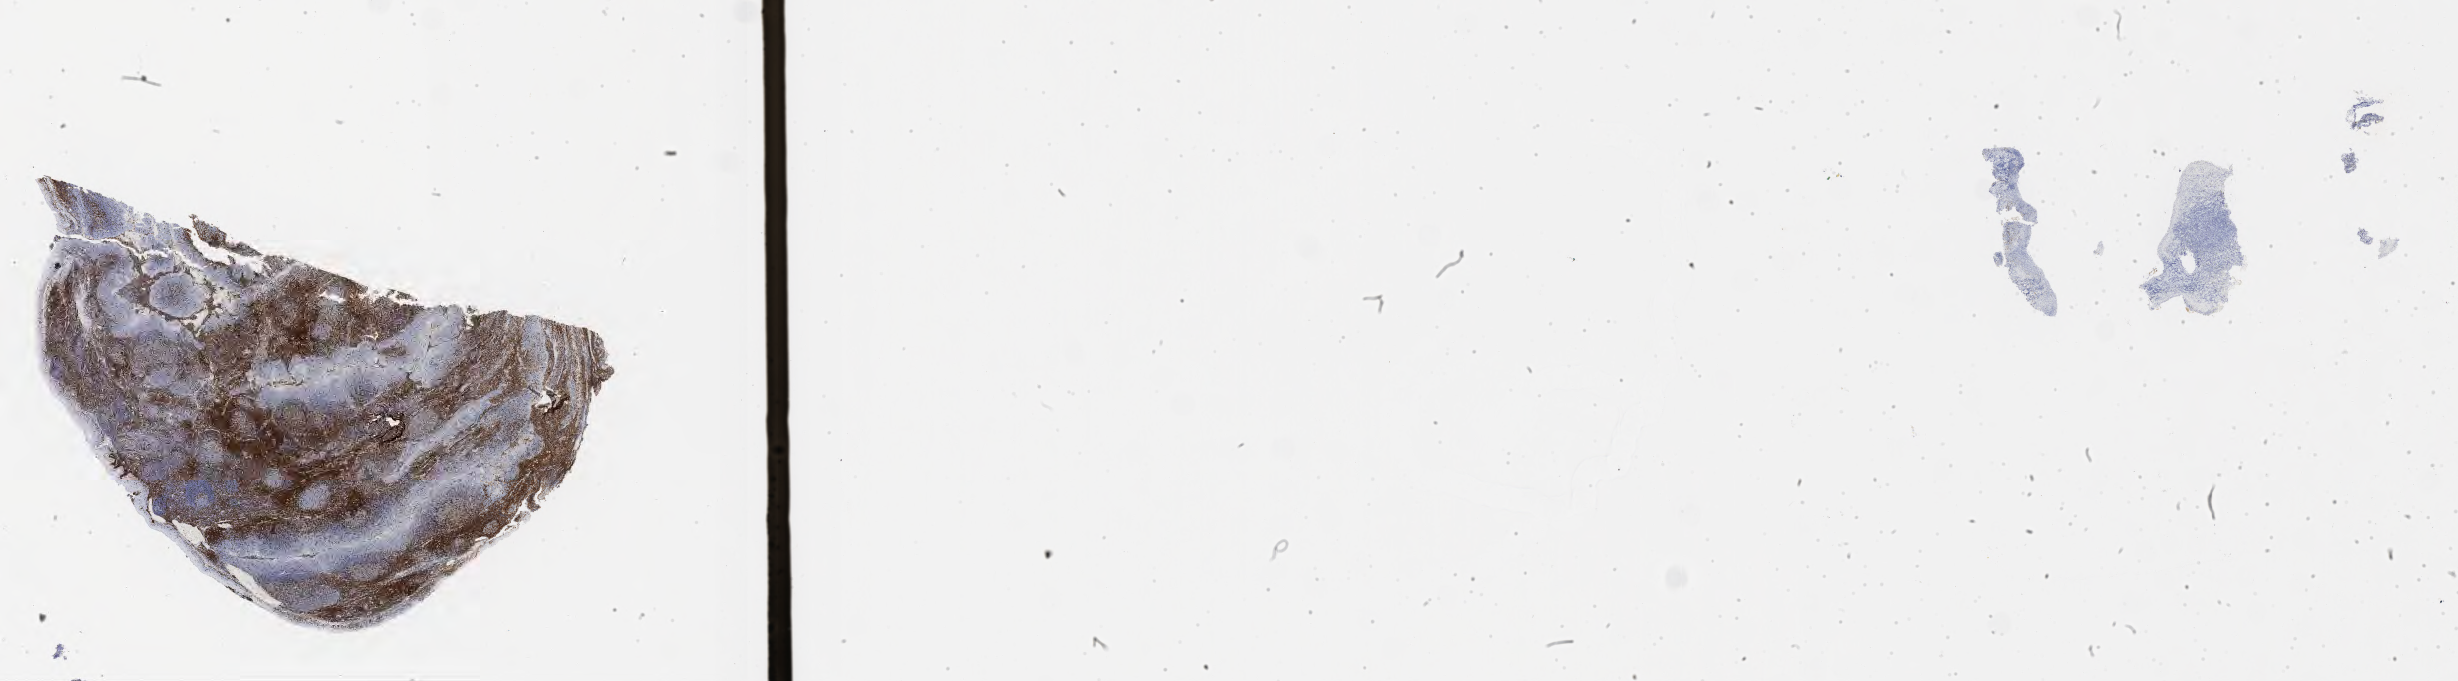
IHC for CD3, whole-slide image, low-resolution overview of the scanned area, about 39.8 x 11.0 mm, specimen: tumor tissue, site: colon. Patient male; aged 28.
Diagnosis: Burkitt lymphoma, NOS.